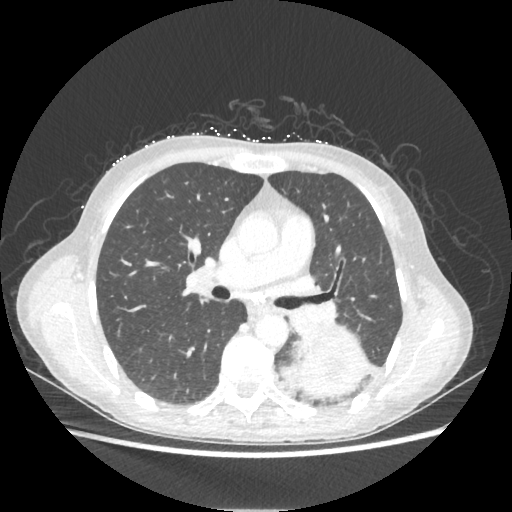
Chest CT, one axial slice. Position 128 of 221 along the scan axis. Lung window (W 1500 / L -600 HU). 1.25 mm slice thickness. 512 × 512 image matrix. Female patient, age 53 years. From the clinical record (not read from this slice): clinical TNM (as recorded): T3 N0 M0.
Structures marked on this image (rectangle marked by the reading radiologist):
- lung tumour (recorded histology: adenocarcinoma): bounding box (x1, y1, x2, y2) in pixels: (294, 325, 368, 398)